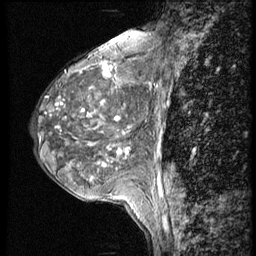
Breast MRI (dynamic contrast-enhanced), one sagittal slice; position 20 of 56 along the scan axis; 4 images stored at this slice position (order not interpretable as contrast timing); 1.5 T; TE 4.2 ms, TR 9 ms; 256 × 256 image matrix. Female patient, age 50 years. Case-level facts recorded for this patient, not image findings: setting: breast cancer imaged before/during neoadjuvant chemotherapy; receptor status: triple-negative.
Outlined on this slice (semi-automatically segmented with operator editing):
- analysis volume of interest (the breast-tissue region the enhancement analysis was run in; not a lesion): bounding box (x1, y1, x2, y2) in pixels: (30, 46, 148, 188)
- tumour enhancement mask (voxels above the 140 % enhancement threshold inside the analysis volume of interest): (56, 49, 122, 166)